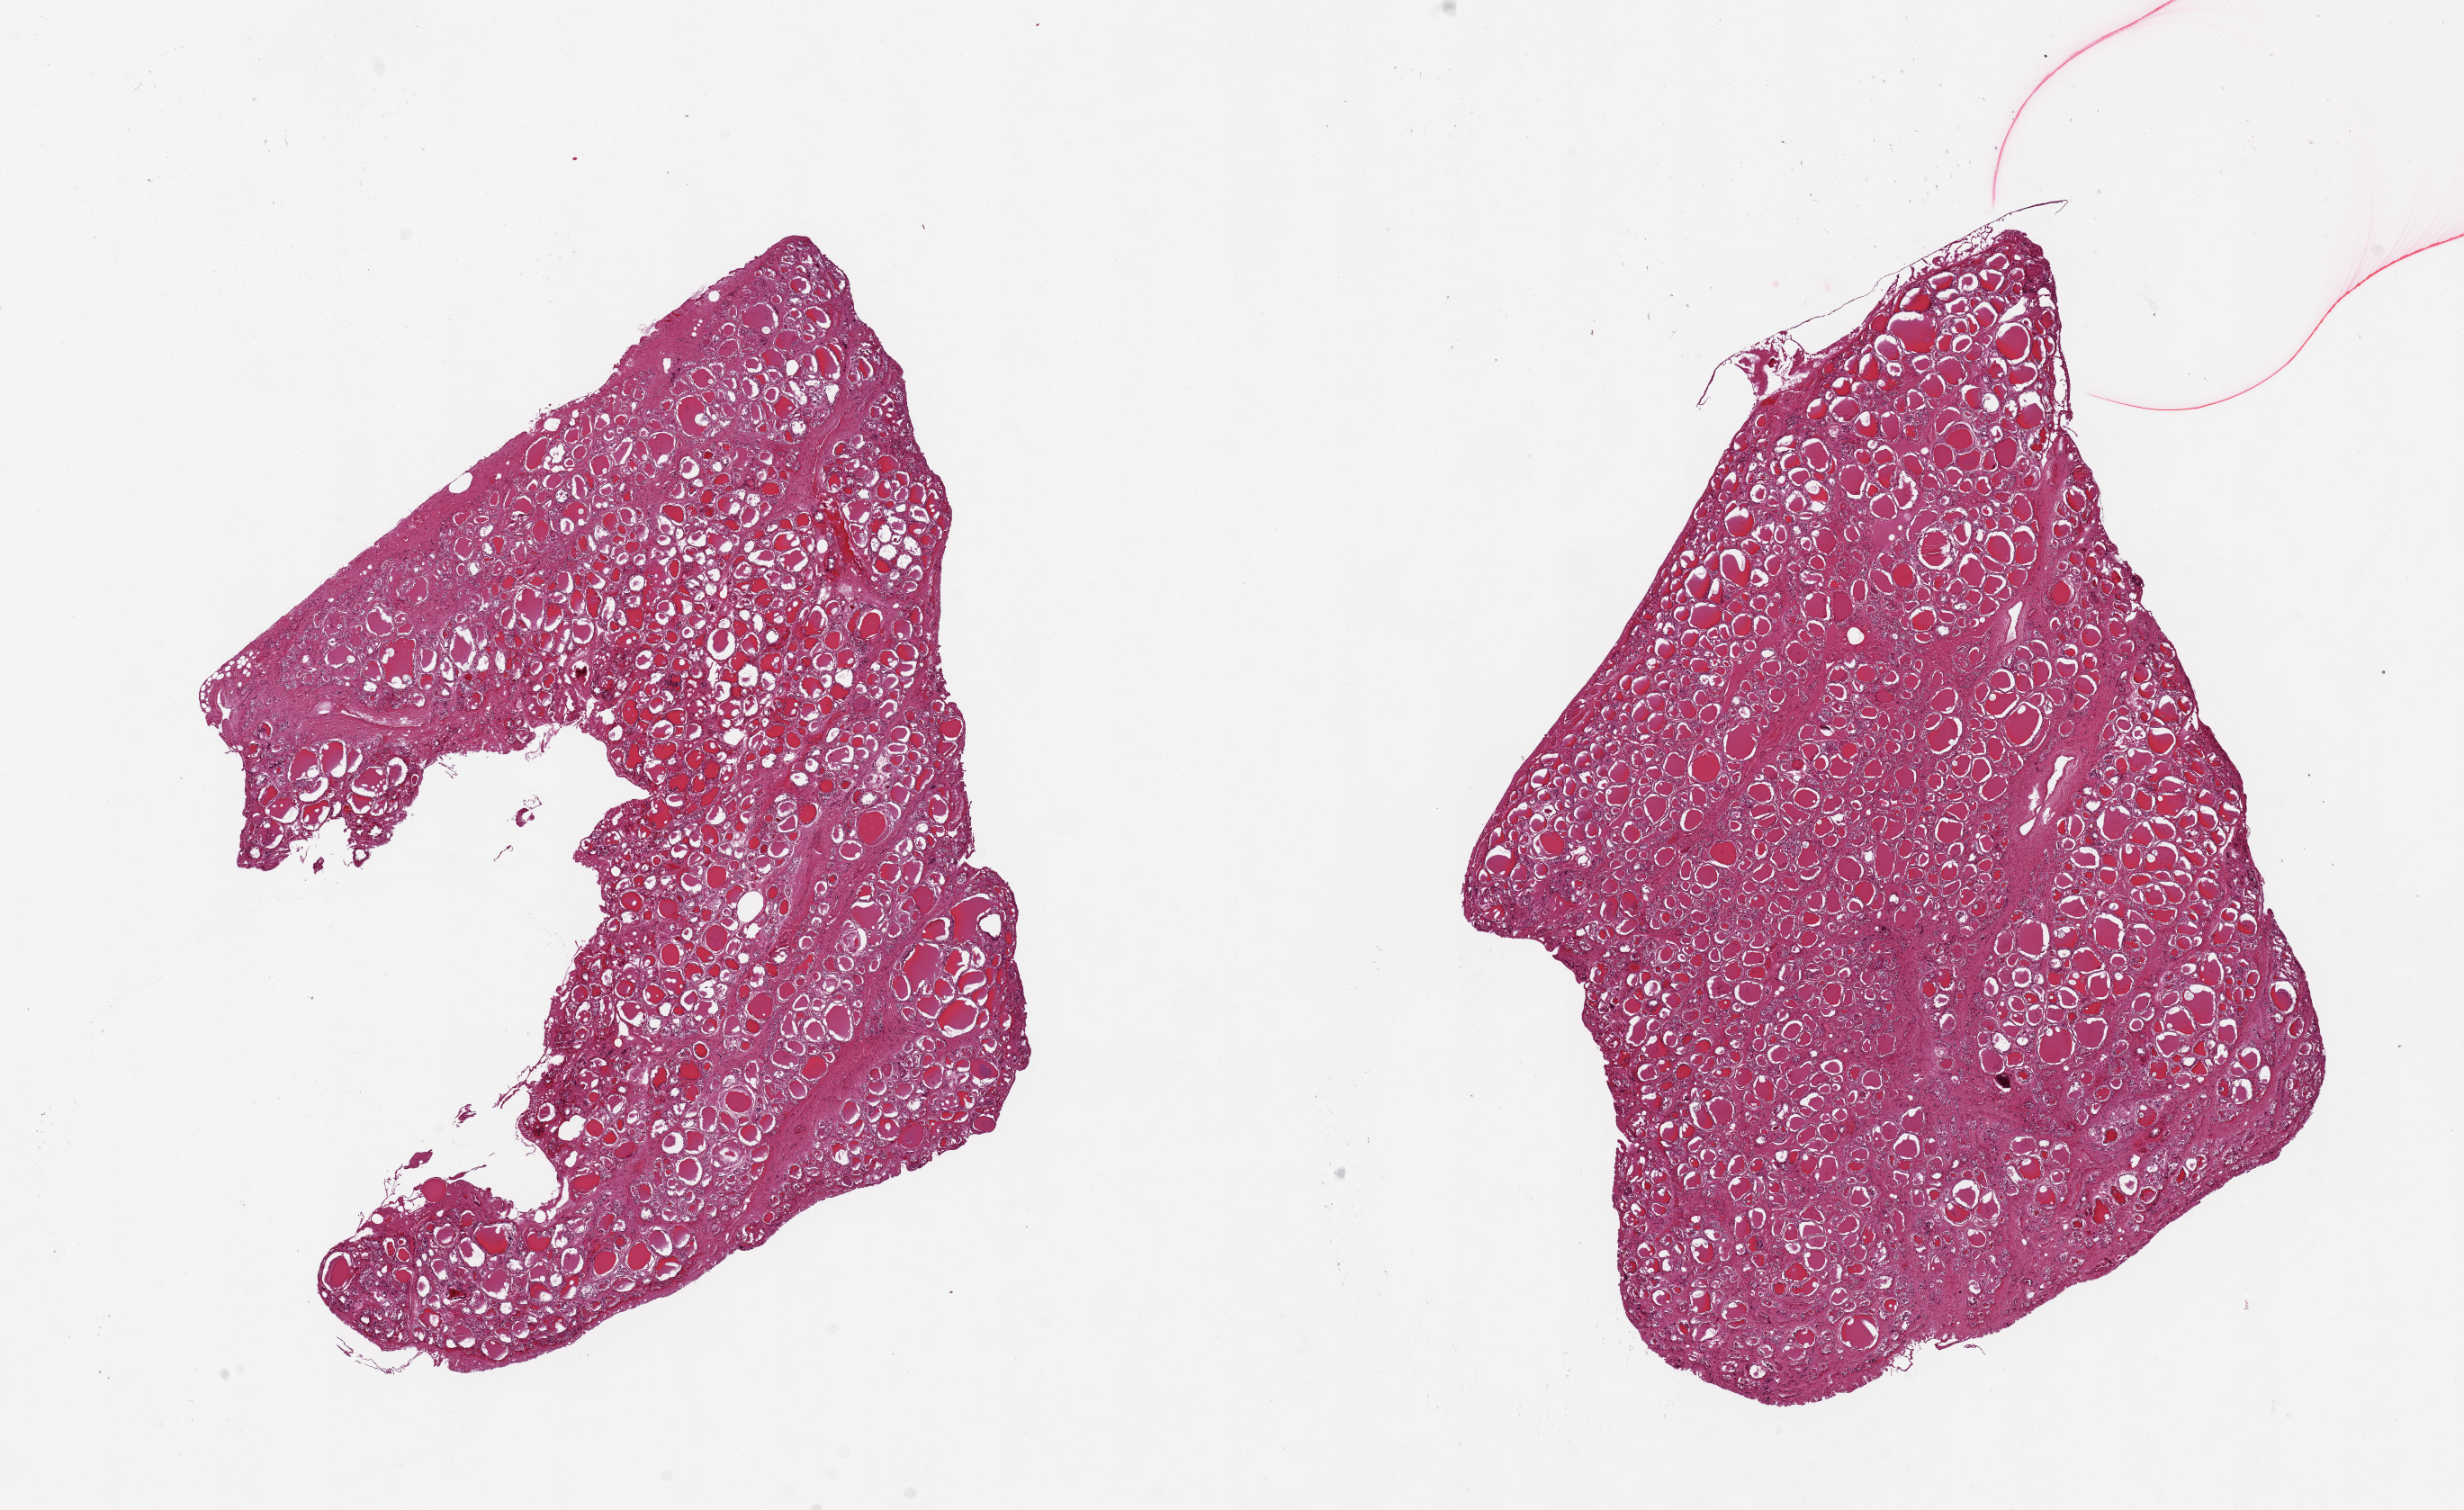
Whole-slide image, haematoxylin and eosin stain — shown as a low-resolution overview of the whole scanned area (about 21.7 x 13.3 mm), PAXgene-fixed paraffin-embedded (PFPE) section, section of thyroid (target tissue), donor tissue sample.
• review note (as recorded): 2 pieces. 8x8 & 9x8mm